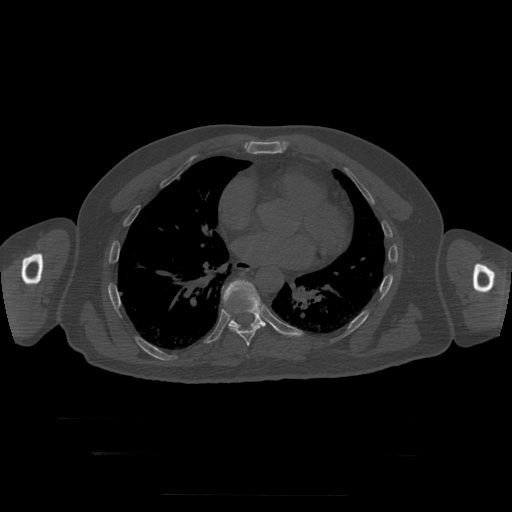
CT including the spine, one axial slice; position 157 of 397 along the scan axis; bone window (W 1800 / L 400 HU); 512 × 512 image matrix, field of view 510 × 510 mm. Patient age 73 years. Case-level facts recorded for this patient, not image findings: primary cancer: prostate.
Annotated regions visible in this slice (semi-automatically segmented with operator editing):
- T8 vertebra: bounding box <223,291,264,347> (left, top, right, bottom; pixels)
- T9 vertebra: <223,280,266,329>